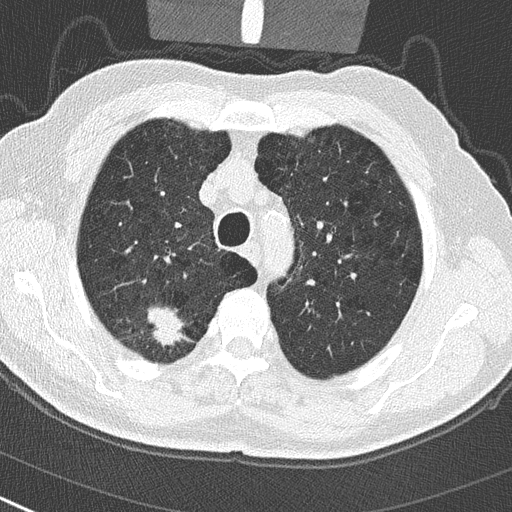
Chest CT (low-dose screening protocol), one axial image; baseline annual screen; lung window (W 1500 / L -600 HU); 2 mm slice thickness; lung (sharp) reconstruction kernel (B50f); slice 64 of 290 in the series; 512 × 512 image matrix, field of view 300 × 300 mm. Male, age 65 years at enrolment. Current smoker at enrolment.
Lesion marked by an expert reader, bounding box <132,301,193,357> (left, top, right, bottom; pixels). Screening reader's record for this exam (one nodule recorded; not confirmed to be the boxed lesion): non-calcified nodule or mass ≥4 mm, right upper lobe, 24 × 19 mm, spiculated (stellate) margins, soft tissue attenuation. Later outcome: lung cancer diagnosed 32 days after this screen — non-small cell carcinoma, right upper lobe, poorly differentiated (G3), stage IA (AJCC 6th edition), 29 mm at pathology.